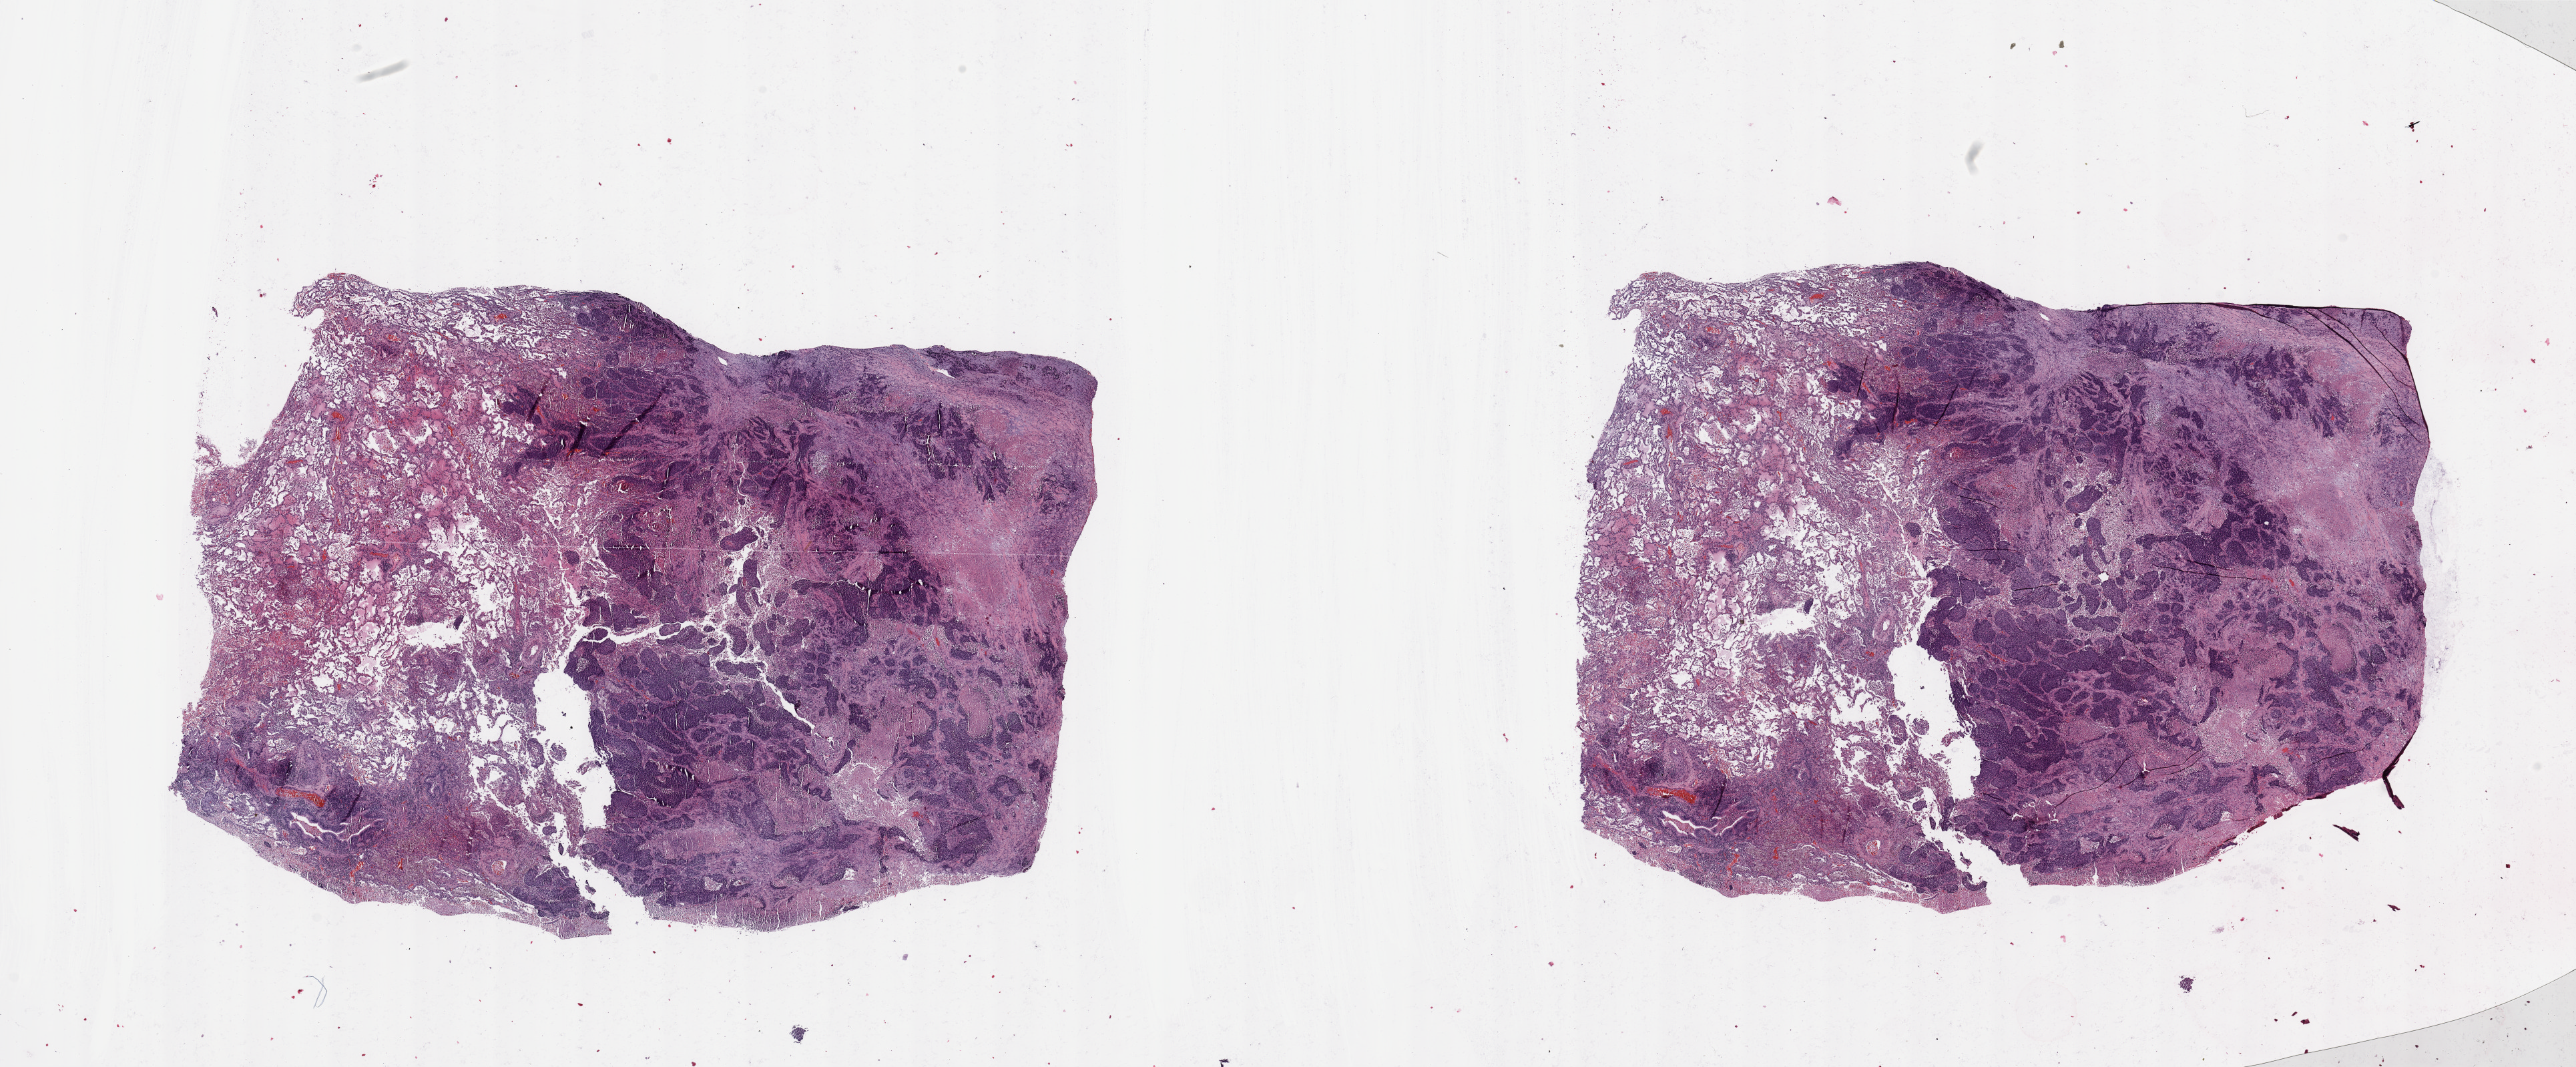
H&E whole-slide image — a low-resolution overview of the entire scanned area, about 30.5 x 12.6 mm. Lung, tumour tissue. 54-year-old male patient. Histologic grade: G2 (moderately differentiated).
AJCC pathologic stage: IIIA. Diagnosis: Squamous cell carcinoma, NOS.